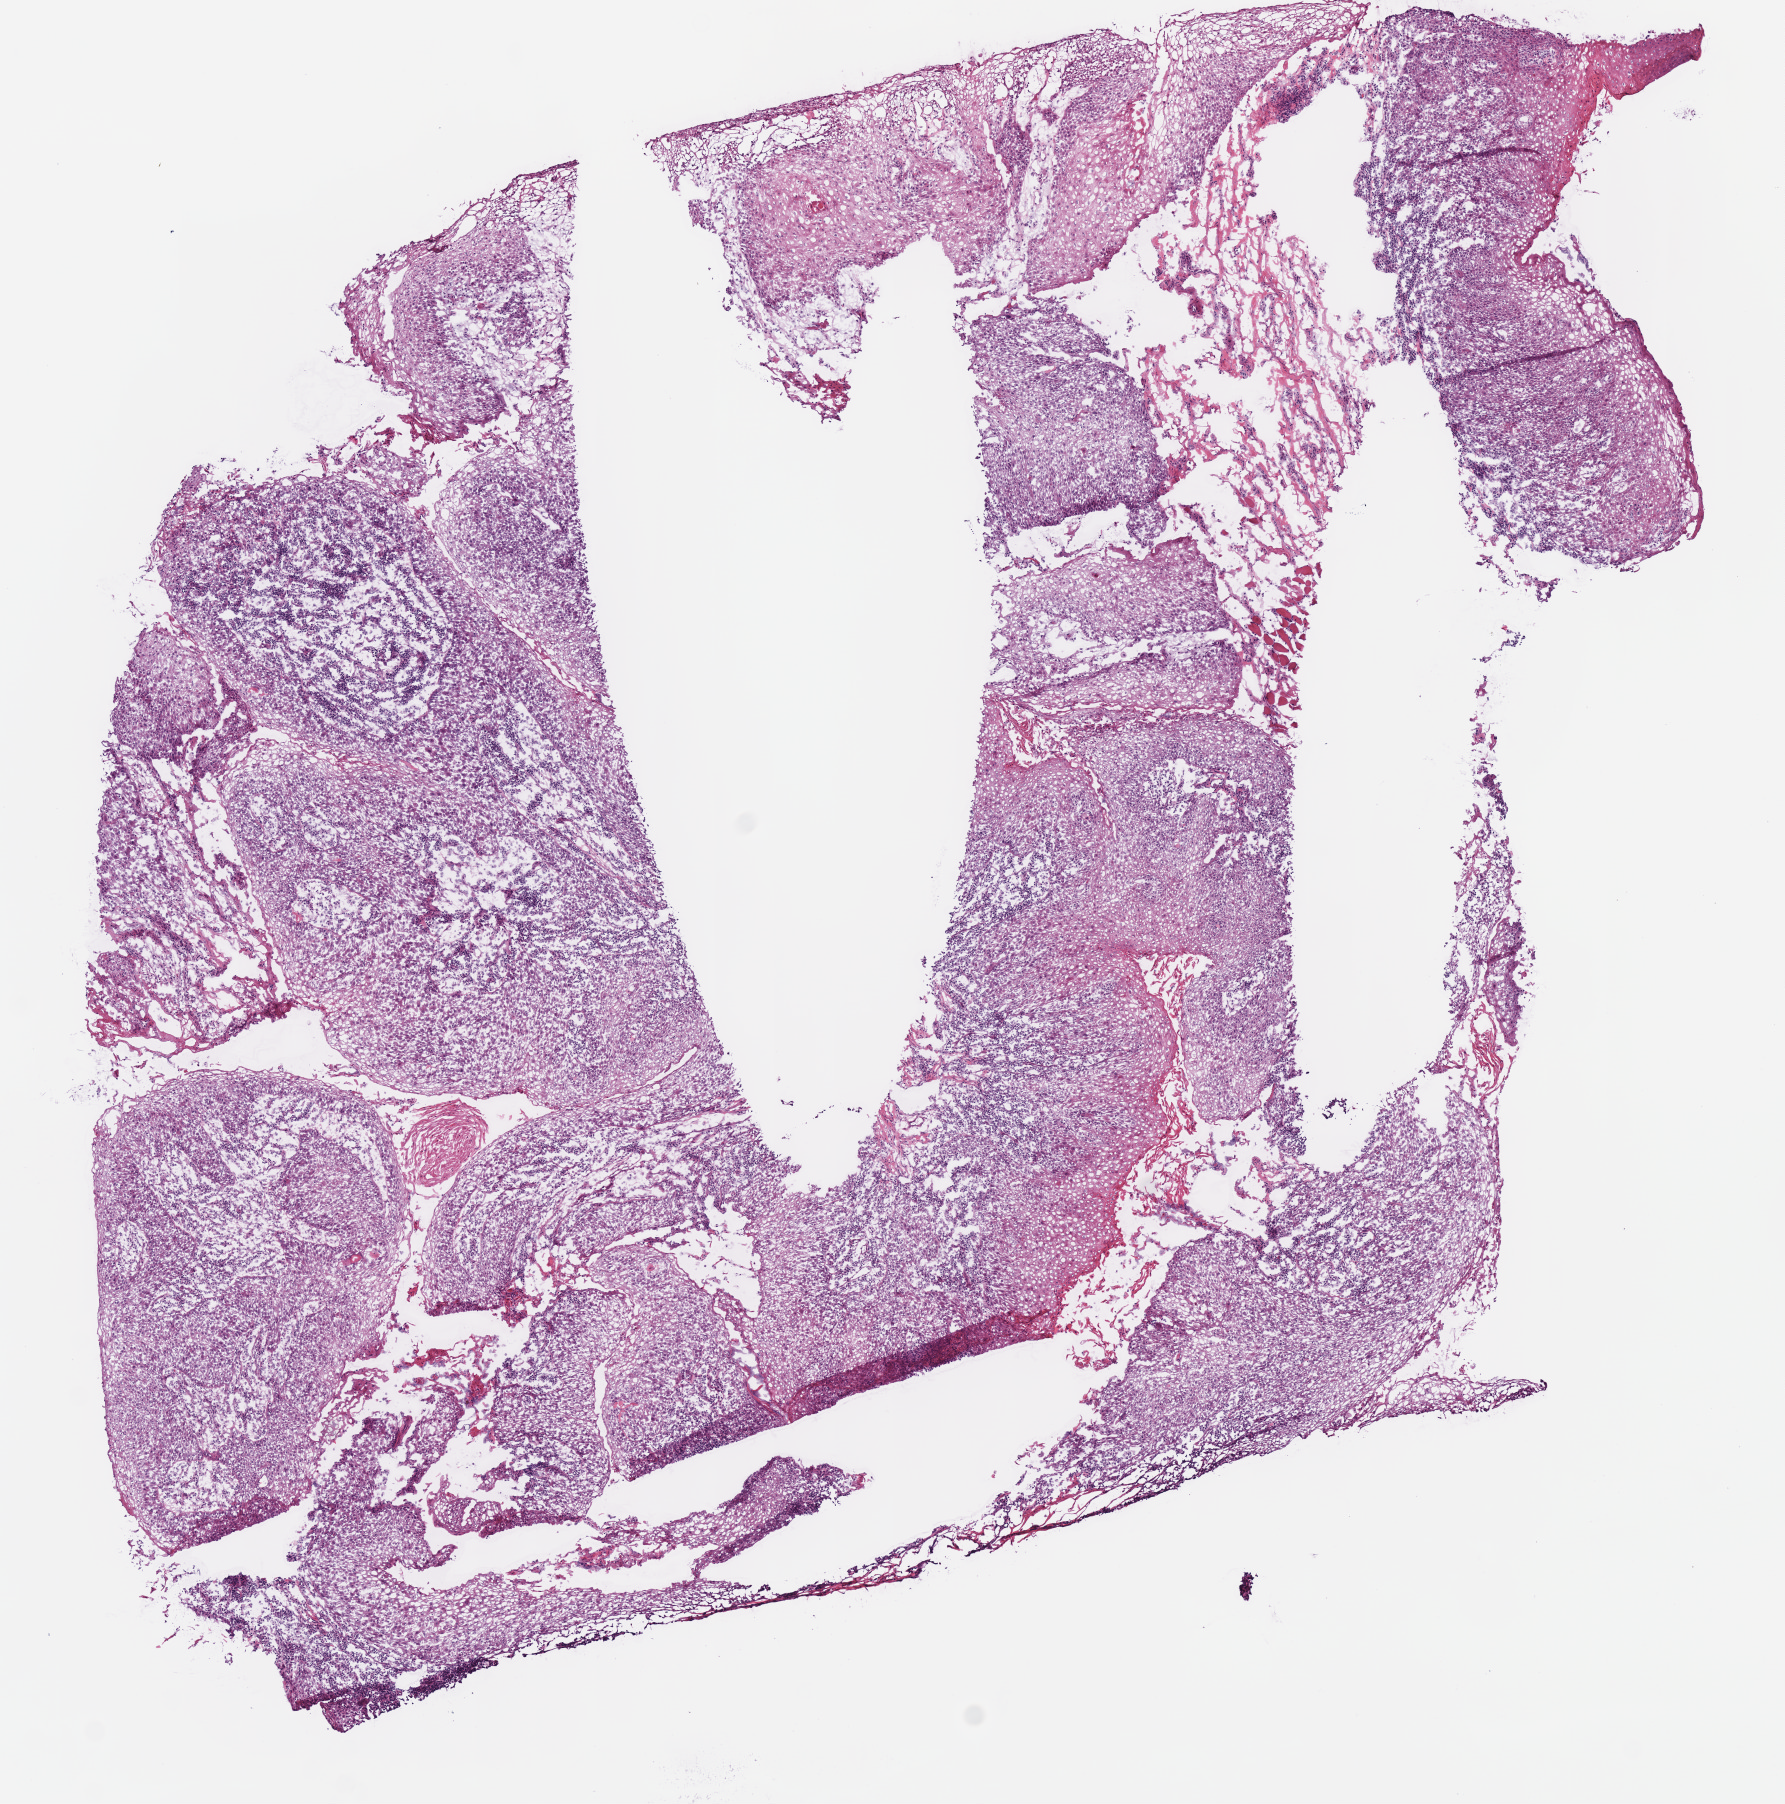
Digitized Hematoxylin and eosin (H&E) stained tissue section (whole slide) — low-resolution overview of the scanned area, about 7.0 x 7.1 mm (acquisition: 40x scan). Frozen section from the bottom of the tissue portion. Sample: primary tumour, head and neck. Female, age 73 years at initial diagnosis. Histologic grade: G1 (well differentiated). Slide review estimates, as recorded: tumour cells 94%, tumour nuclei 71%, normal cells 6%, stromal cells 0%, necrosis 0%. Inflammatory infiltration, as recorded: lymphocyte infiltration 20%, monocyte infiltration 0%, neutrophil infiltration 0%.
* AJCC pathologic stage: II (7th edition)
* diagnosis: Squamous cell carcinoma, NOS